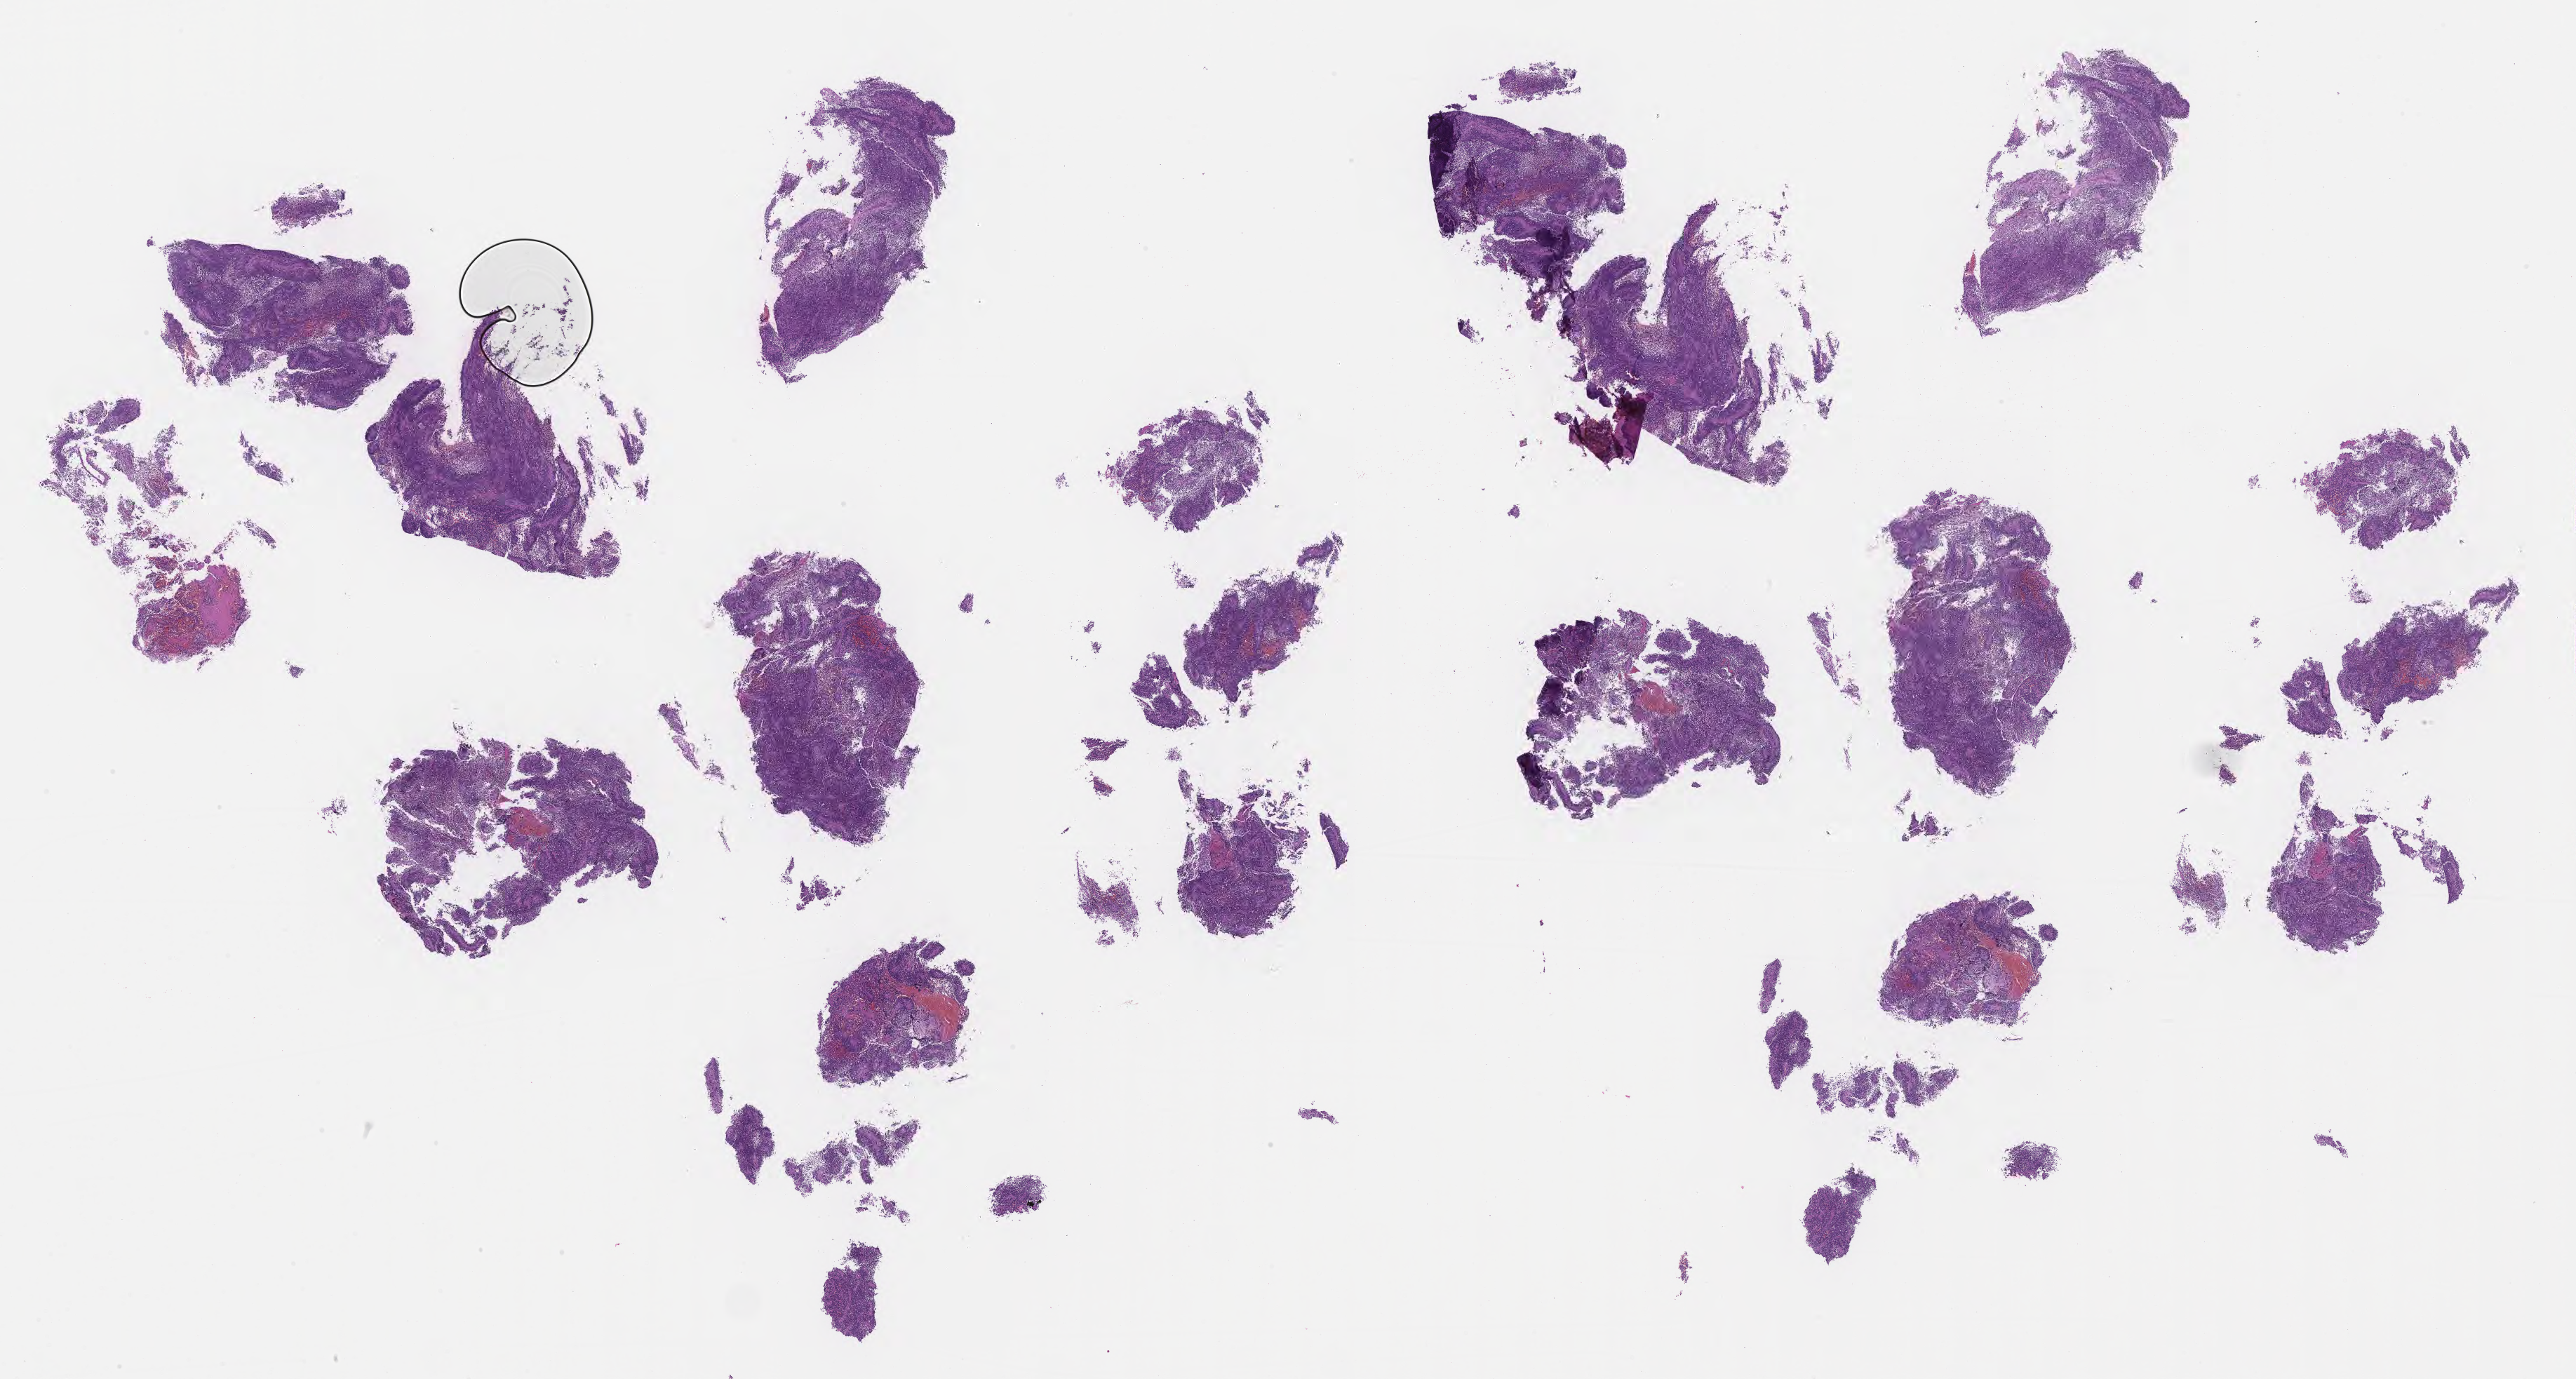
Digitized haematoxylin and eosin-stained section of tumor tissue from the spinal cord — shown as a low-resolution overview of the whole scanned area (about 29.7 x 15.9 mm); formalin-fixed paraffin-embedded section. Patient: female, age 100 months.
Diagnosis: Glioma, malignant.